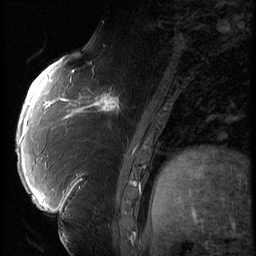
Breast MRI (dynamic contrast-enhanced), one sagittal slice; position 25 of 66 along the scan axis; 3 images stored at this slice position (order not interpretable as contrast timing); 1.5 T; TE 4.2 ms, TR 9 ms; 2.5 mm slice thickness; 256 × 256 image matrix, field of view 180 × 180 mm. Patient: female, 57 years. From the clinical record (not read from this slice): setting: breast cancer imaged before/during neoadjuvant chemotherapy; receptor status: triple-negative.
Structures marked on this image (semi-automatic segmentation, software-assisted and operator-edited):
- analysis volume of interest (the breast-tissue region the enhancement analysis was run in; not a lesion): bounding box <86,74,138,129> (left, top, right, bottom; pixels)
- tumour enhancement mask (voxels above the 140 % enhancement threshold inside the analysis volume of interest): <86,88,123,123>